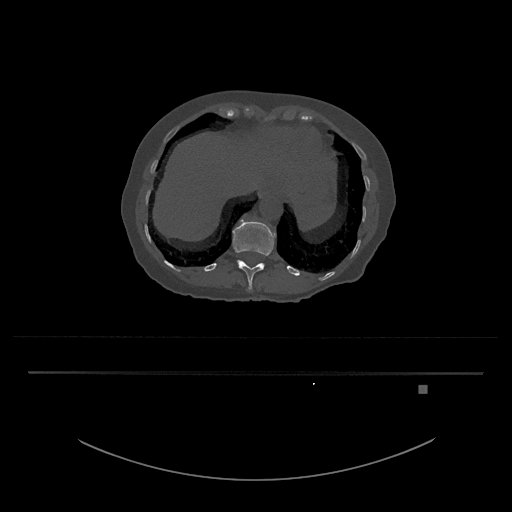
CT including the spine, one axial slice. Slice 605 of 797 in the series (ordered by position). 120 kVp. Bone window (W 1800 / L 400 HU). 0.5 mm slice thickness. 512 × 512 image matrix. Female patient, age 57 years. From the clinical record (not read from this slice): primary cancer: cervical.
Outlined on this slice (semi-automatic segmentation, software-assisted and operator-edited):
- T12 vertebra: bounding box <232,219,276,290> (left, top, right, bottom; pixels)